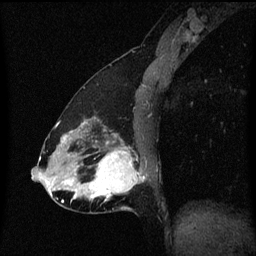
Breast MRI (dynamic contrast-enhanced), one sagittal slice. Position 26 of 60 along the scan axis. Dynamic contrast-enhanced series, image 2 of 3 at this slice position (ordered by acquisition). 1.5 T. TE 4.2 ms, TR 8.4 ms. 256 × 256 image matrix. Female patient, age 47 years.
Outlined on this slice (semi-automatically segmented with operator editing):
- analysis volume of interest (the breast-tissue region the enhancement analysis was run in; not a lesion): bounding box [x1, y1, x2, y2] px = [81, 138, 145, 213]
- tumour enhancement mask (voxels above the 70 % enhancement threshold inside the analysis volume of interest): [88, 142, 143, 201]